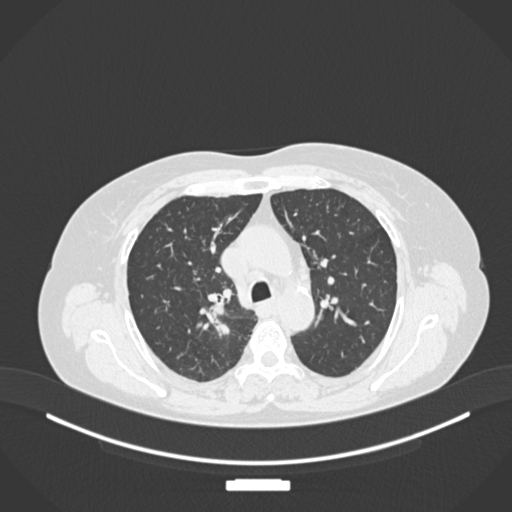
Chest CT, one axial slice; position 177 of 237 along the scan axis; reconstruction kernel B30f; lung window (W 1500 / L -600 HU); 1 mm slice thickness; 512 × 512 image matrix, field of view 400 × 400 mm. Female patient, age 62 years. From the clinical record (not read from this slice): clinical TNM (as recorded): T1c N1 M0.
Outlined on this slice (rectangle marked by the reading radiologist):
- lung tumour (recorded histology: squamous cell carcinoma): bounding box (x1, y1, x2, y2) in pixels: (205, 296, 233, 339)